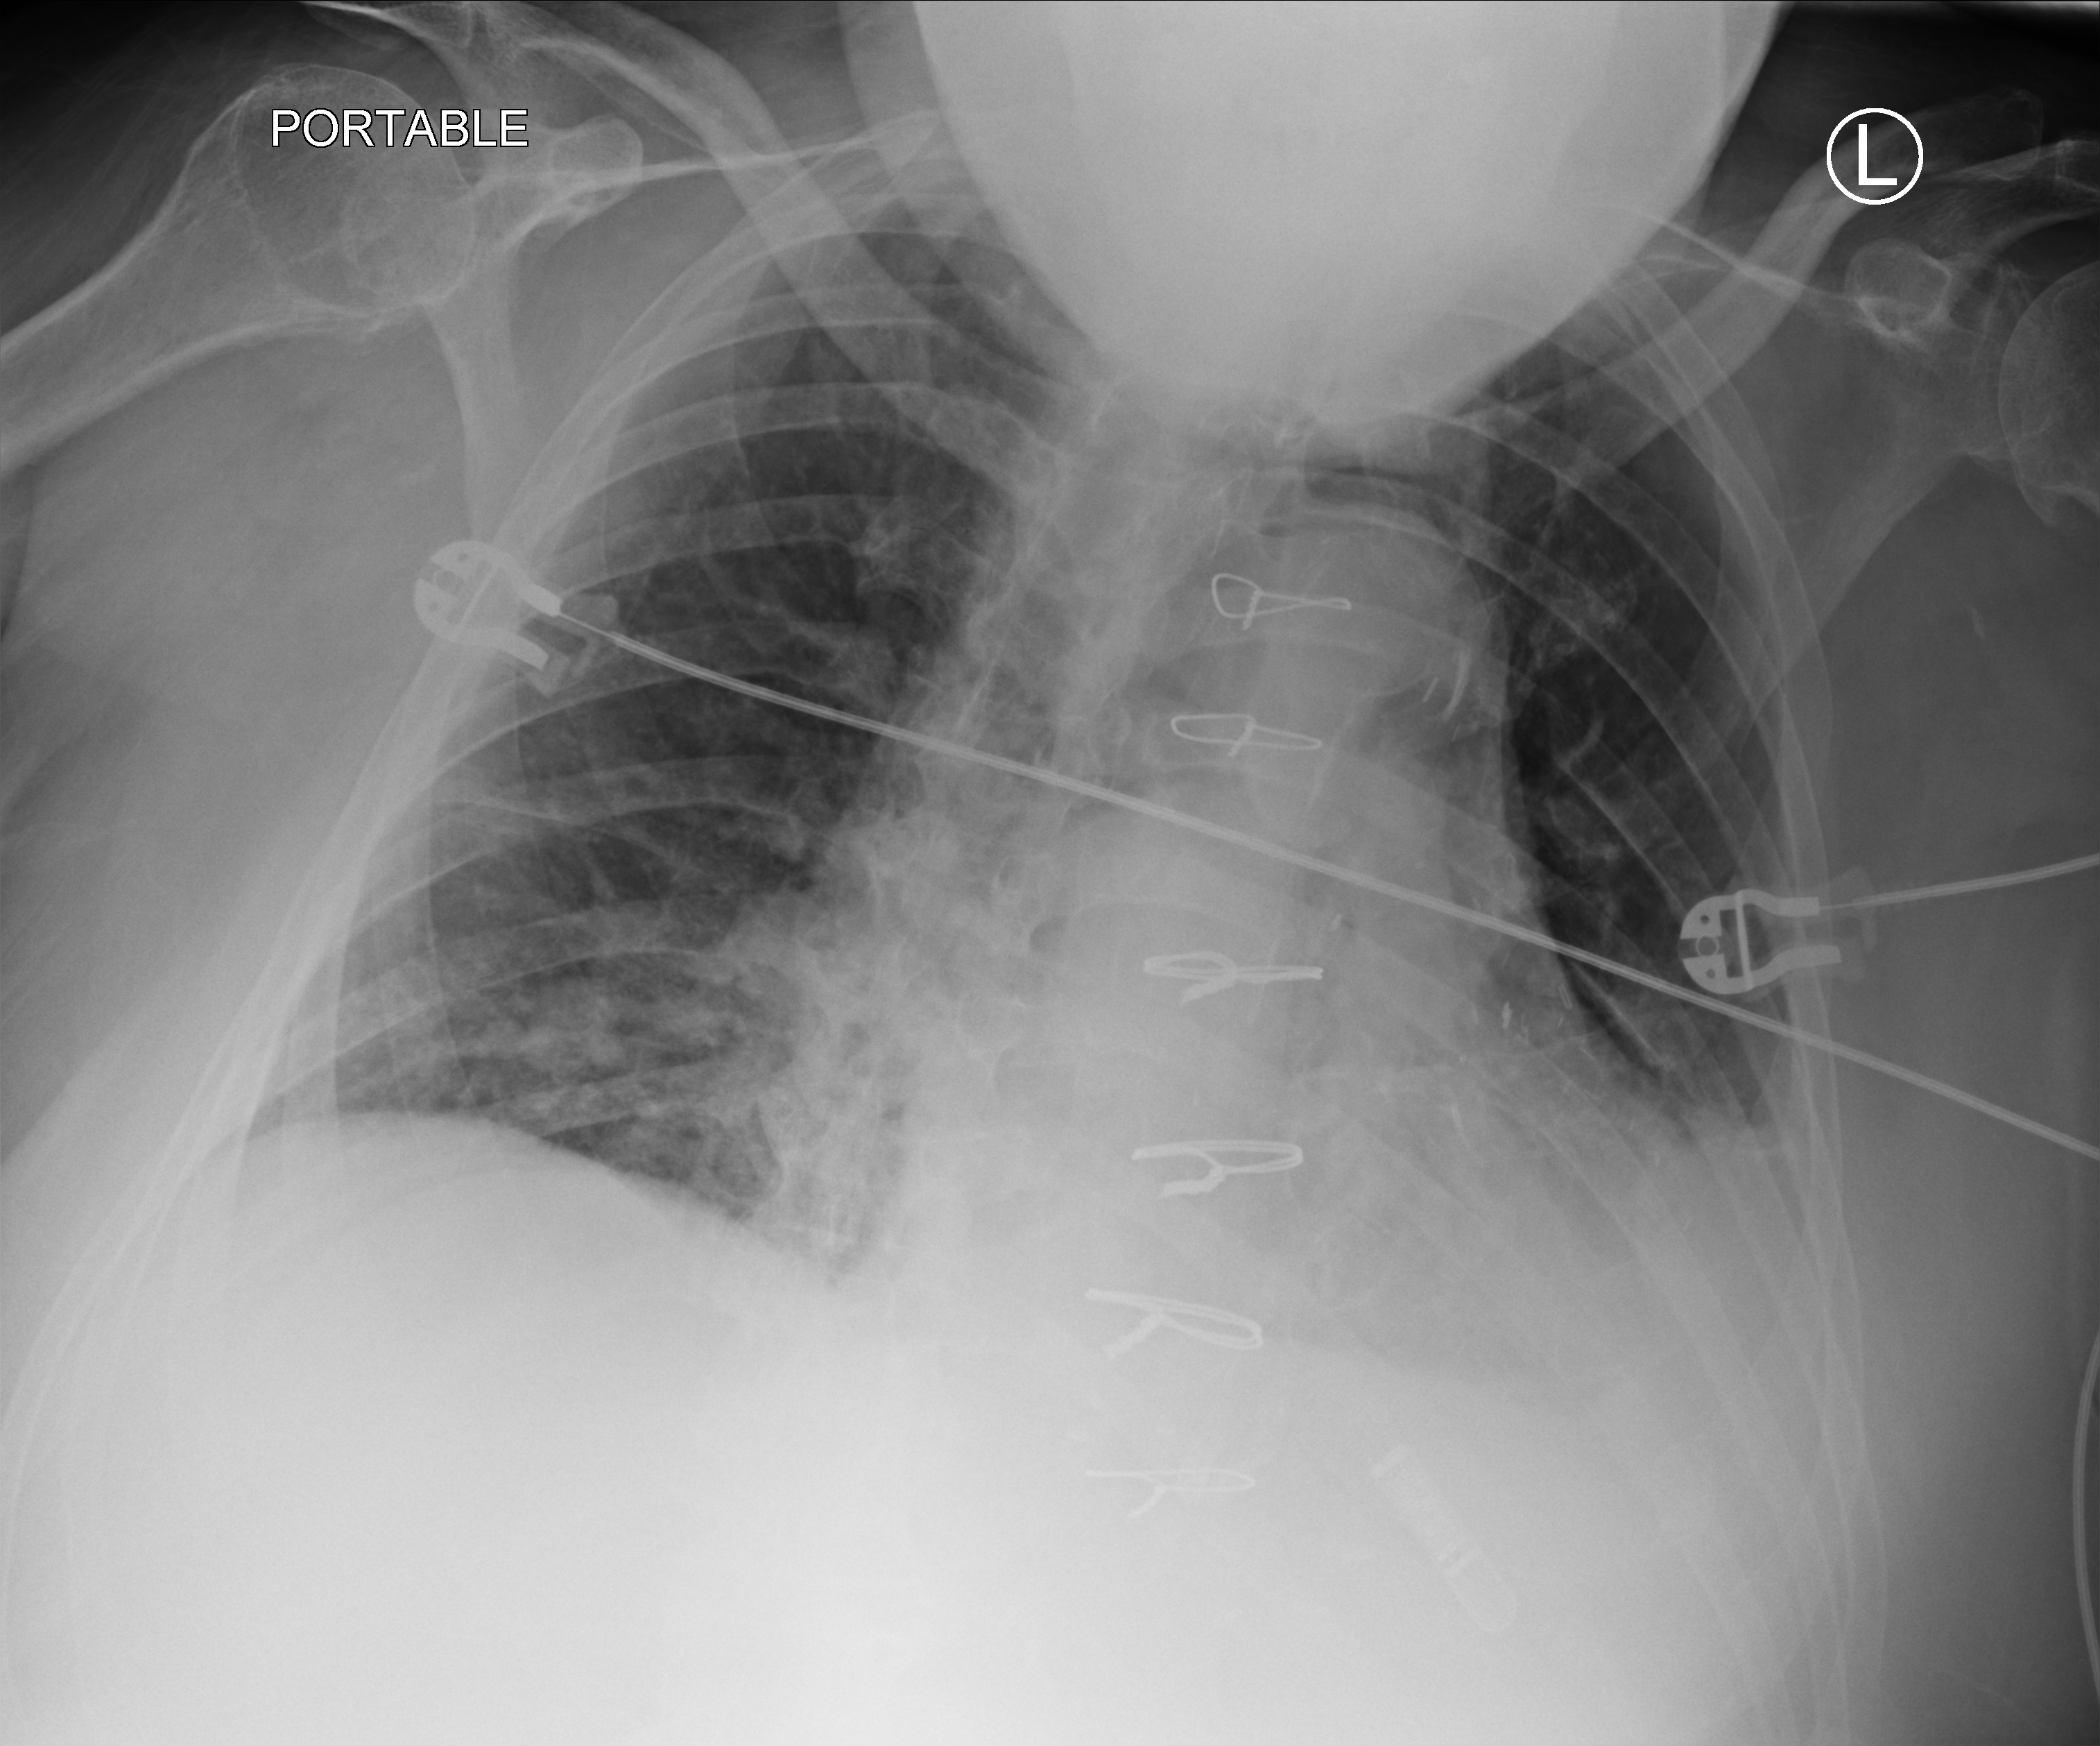
Portable chest radiograph; anteroposterior (AP) projection. Male patient hospitalised with COVID-19, age 60–74 years.
Hospital-stay facts (about this admission, not read from this image; timing relative to this image not recorded):
- other chronic lung disease (admission record): no
- COPD (admission record): no
- admitted to intensive care during this hospital stay: no